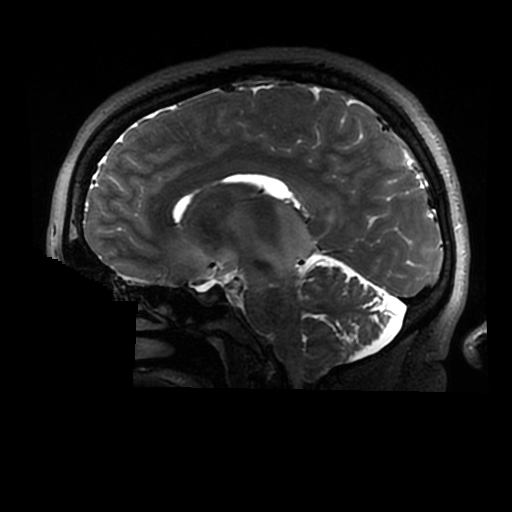
Brain MRI from a brain-tumour surgery series, one sagittal slice; slice 168 of 320 in the series (ordered by position); 512 × 512 image matrix, field of view 240 × 240 mm. Case-level facts recorded for this patient, not image findings: histopathology: Astrocytoma; WHO grade: 2; IDH mutation: yes.
Outlined on this slice (manually delineated by an expert):
- tumour: bounding box (x1, y1, x2, y2) in pixels: (205, 202, 316, 278)